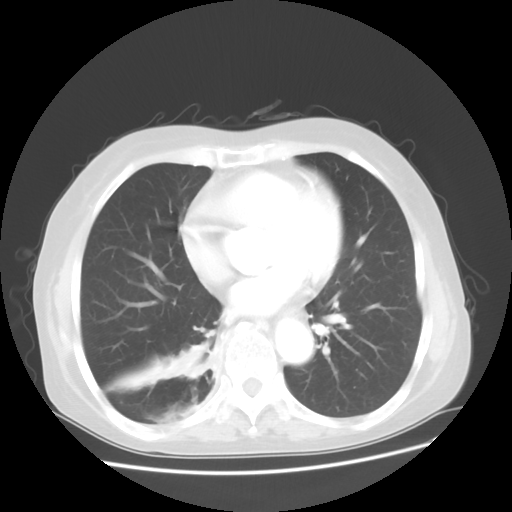
Chest CT, one axial slice; reconstruction kernel STANDARD; 120 kVp; lung window (W 1500 / L -600 HU); 5 mm slice thickness; 512 × 512 image matrix, field of view 360 × 360 mm. Patient: female, 63 years. From the clinical record (not read from this slice): clinical TNM (as recorded): T2 N3 M1b; histopathological grade: G3.
Structures marked on this image (bounding box drawn by a radiologist):
- lung tumour (recorded histology: small cell carcinoma): bounding box <176,336,215,378> (left, top, right, bottom; pixels)